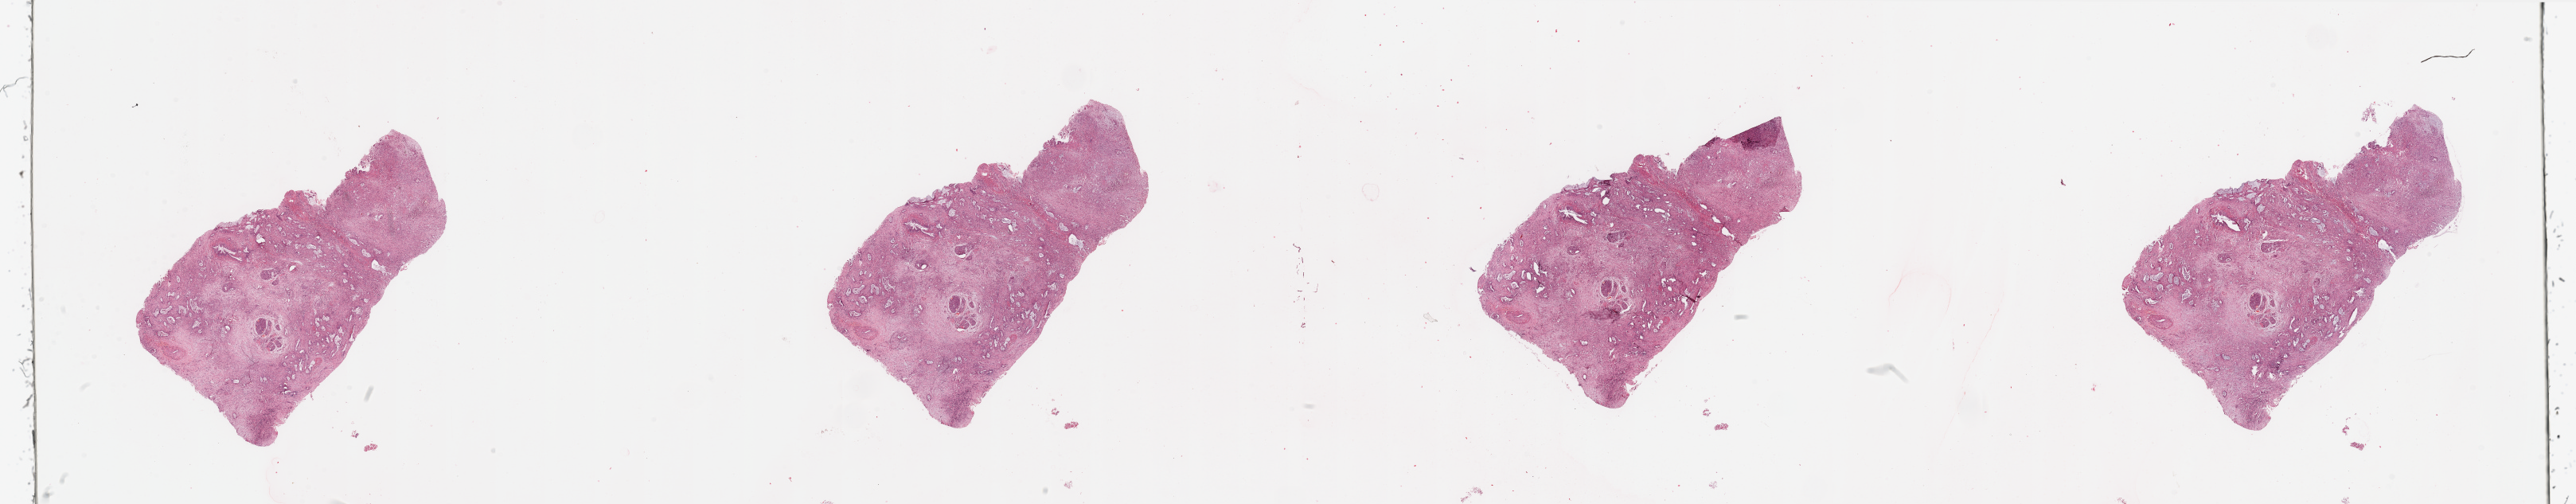
Digitized H&E-stained tissue section (whole slide), shown as a low-resolution overview of the whole scanned area (about 51.2 x 10.0 mm, slide scanned at 20x). Tumour tissue sample, sampled site: pancreas. 72-year-old male patient. Histologic grade: G2 (moderately differentiated). Slide review estimates, as recorded: tumour nuclei 20%, necrosis 0%.
AJCC pathologic stage: IB. Diagnosis: Infiltrating duct carcinoma, NOS.